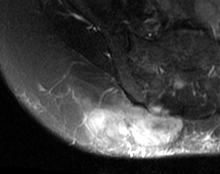
MRI of an extremity soft-tissue mass, one axial slice; T2-weighted fat-saturated; MR volume resampled by the dataset authors to the PET/CT grid (not the native acquisition matrix); 220 × 174 image matrix, field of view 215 × 170 mm. Female patient. Case-level facts recorded for this patient, not image findings: histological type: spindle cell suggestive of myxofibrosarcoma; grade: intermediate; site of the primary tumour: right buttock.
Outlined on this slice (expert contour drawn on MRI and transferred to this co-registered scan by the dataset authors):
- gross tumour volume (mass): box from (x=84, y=97) to (x=183, y=149) px